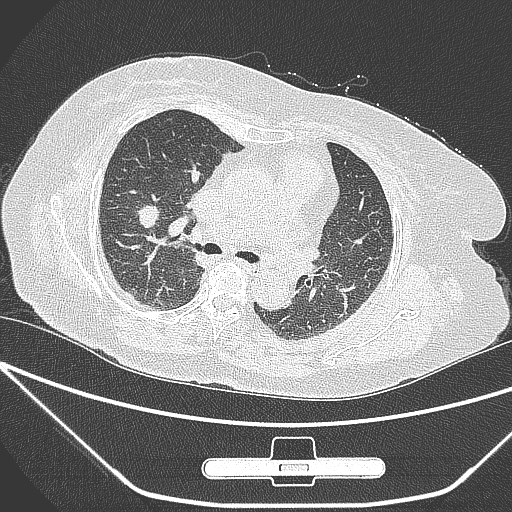
Chest CT, one axial slice; position 163 of 245 along the scan axis; 120 kVp; lung window (W 1500 / L -600 HU); 1 mm slice thickness; 512 × 512 image matrix, field of view 365 × 365 mm. Patient: female, 65 years. From the clinical record (not read from this slice): clinical TNM (as recorded): T1c N0 M0.
Annotated regions visible in this slice (bounding box drawn by a radiologist):
- lung tumour (recorded histology: adenocarcinoma): box from (x=133, y=196) to (x=165, y=234) px